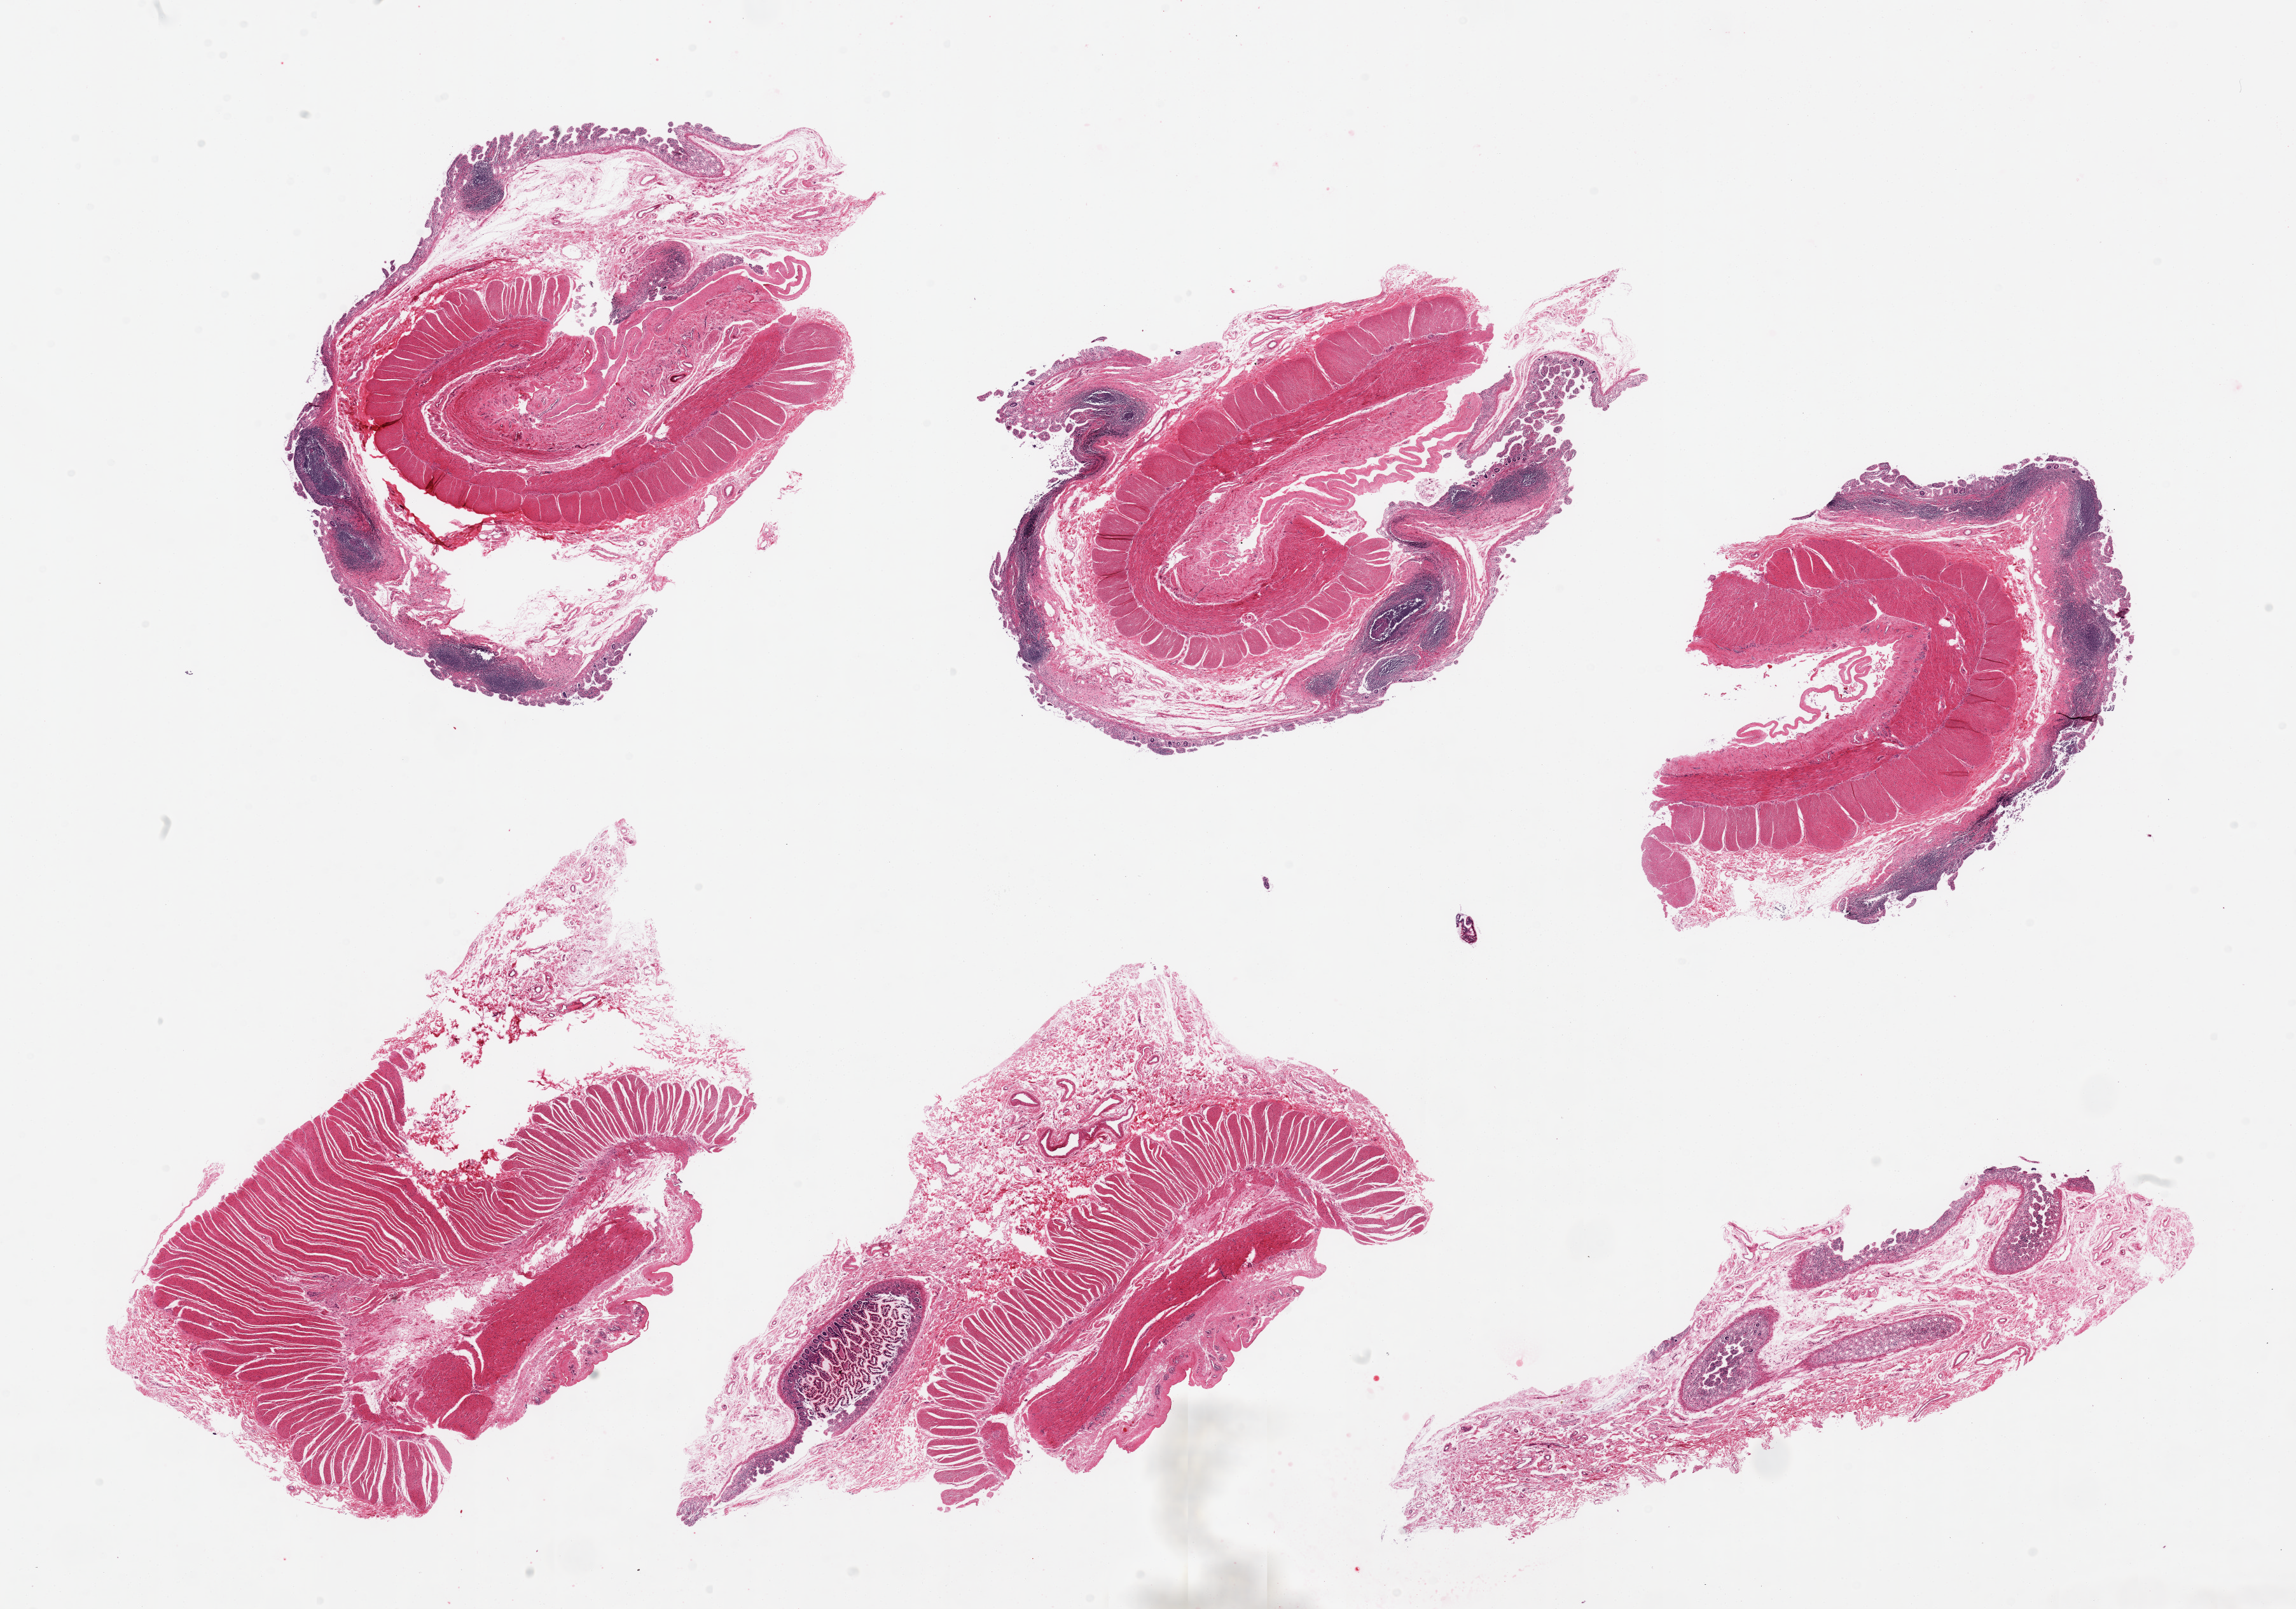
Digitized hematoxylin and eosin (H&E)-stained section, brightfield — a low-resolution overview of the entire scanned area, about 28.5 x 20.0 mm. PAXgene-fixed paraffin-embedded (PFPE) section. Target tissue: ileum. Donor tissue sample.
Reviewer comment on this tissue sample: 6 pieces; moderately to severely autolyzed mucosa and 3 of 6 pieces contain preserved lymphoid aggregates.